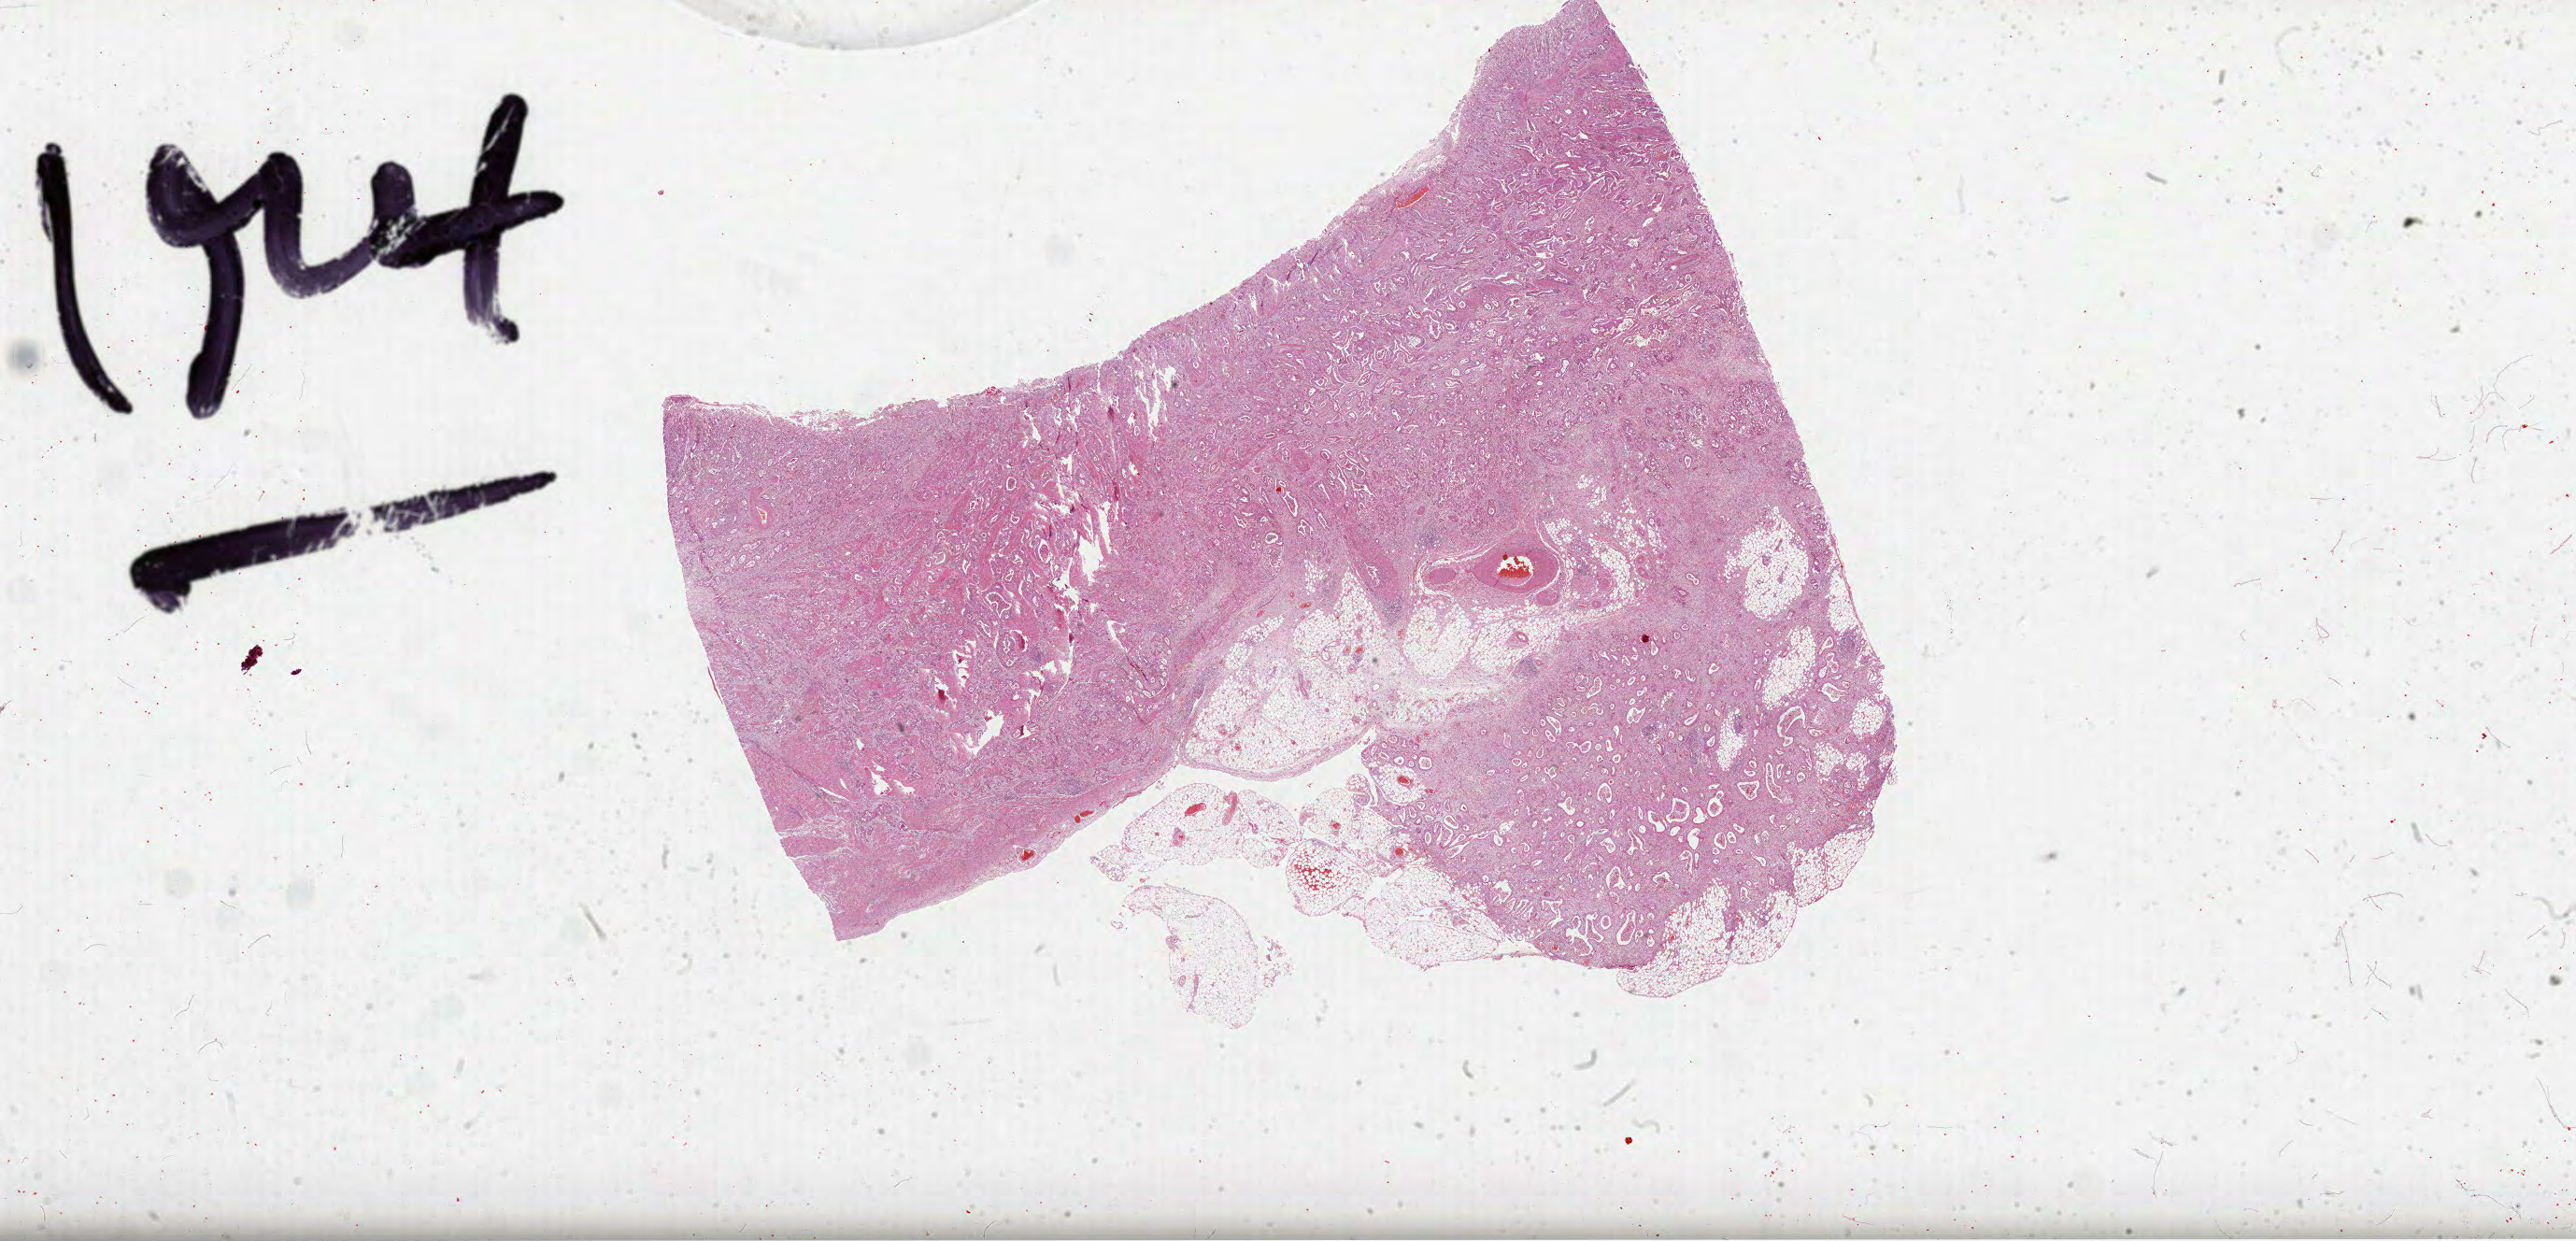
Whole-slide histology image, H&E-stained — a low-resolution overview of the entire scanned area, about 44.5 x 21.4 mm (slide scanned at 40x), FFPE section, stomach, primary tumour sample. Female, age 67 years at initial diagnosis. Histologic grade: G2 (moderately differentiated).
Lymph nodes positive (case pathology): 3 of 19 examined. Histologic diagnosis: Tubular adenocarcinoma. AJCC pathologic stage: IIIA (7th edition).